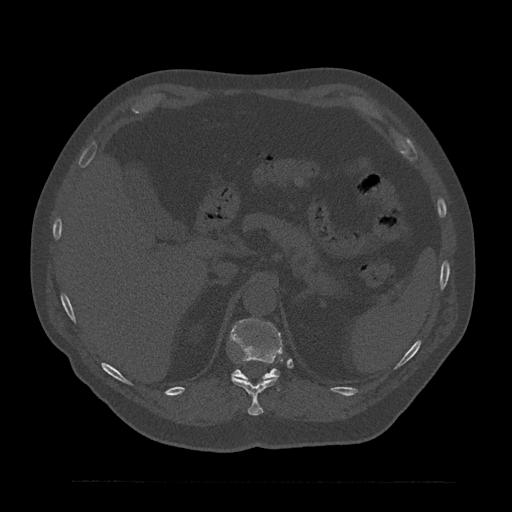
CT including the spine, one axial slice. Position 263 of 797 along the scan axis. Bone window (W 1800 / L 400 HU). 0.5 mm slice thickness. 512 × 512 image matrix, field of view 430 × 430 mm. Patient: male, 61 years. Case-level facts recorded for this patient, not image findings: primary cancer: prostate.
Annotated regions visible in this slice (semi-automatically segmented with operator editing):
- T11 vertebra: bounding box <231,375,278,416> (left, top, right, bottom; pixels)
- T12 vertebra: <230,319,283,390>